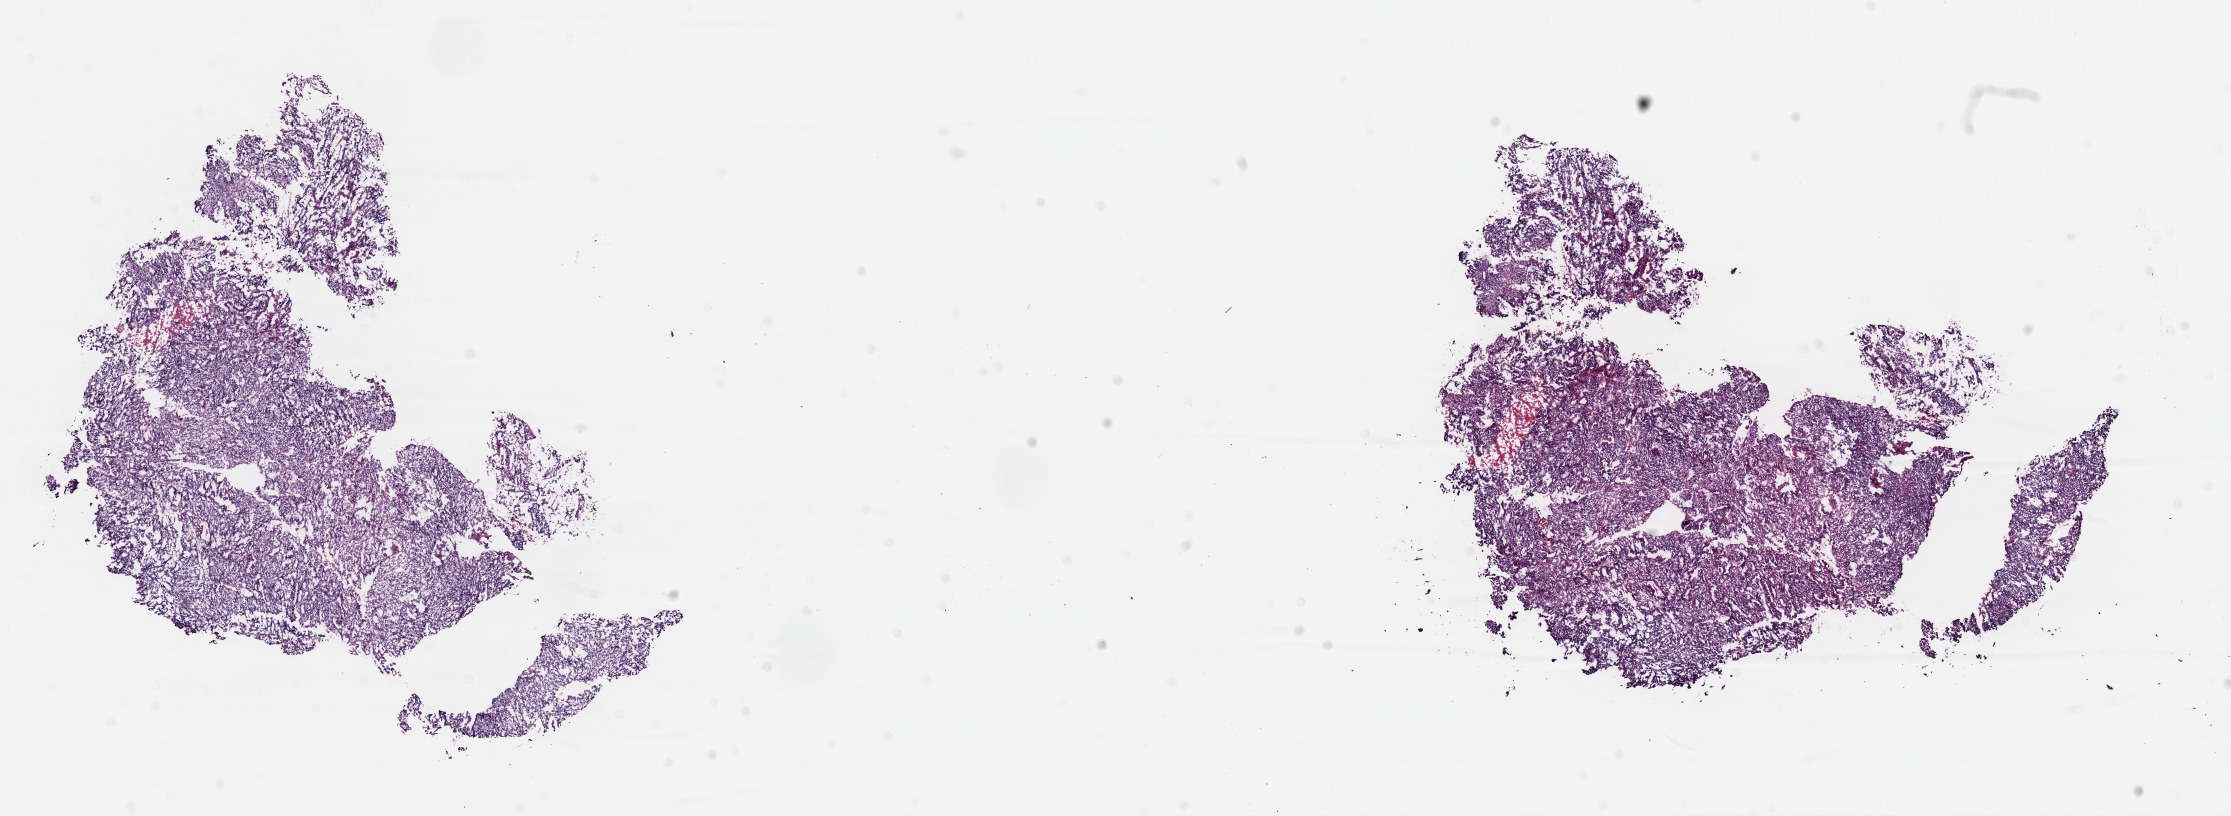
H&E-stained whole-slide image, a low-resolution overview of the entire scanned area, about 17.6 x 6.4 mm (acquisition: 40x scan), frozen section, sample: primary tumour, uterus. Patient: female, age at initial diagnosis 76 years. Histologic grade: G3 (poorly differentiated). Pathologist review of this section (percent, as recorded): tumour cells 96%, tumour nuclei 97%, normal cells 0%, stromal cells 2%, necrosis 2%. Infiltration values recorded for this section: lymphocyte infiltration 1%, monocyte infiltration 0%, neutrophil infiltration 0%.
- FIGO stage: IA
- diagnosis: Endometrioid adenocarcinoma, NOS (endometrium)